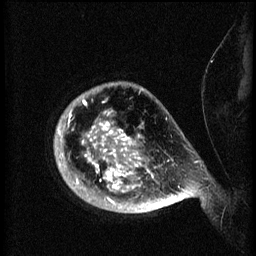
Breast MRI (dynamic contrast-enhanced), one sagittal slice. Slice 57 of 60 in the series (ordered by position). 3 images stored at this slice position (order not interpretable as contrast timing). 1.5 T. TE 4.2 ms, TR 8.2 ms. 2 mm slice thickness. 256 × 256 image matrix. Female patient, age 50 years.
Structures marked on this image (semi-automatic segmentation, software-assisted and operator-edited):
- analysis volume of interest (the breast-tissue region the enhancement analysis was run in; not a lesion): bounding box <55,84,173,213> (left, top, right, bottom; pixels)
- tumour enhancement mask (voxels above the 70 % enhancement threshold inside the analysis volume of interest): <58,100,173,209>